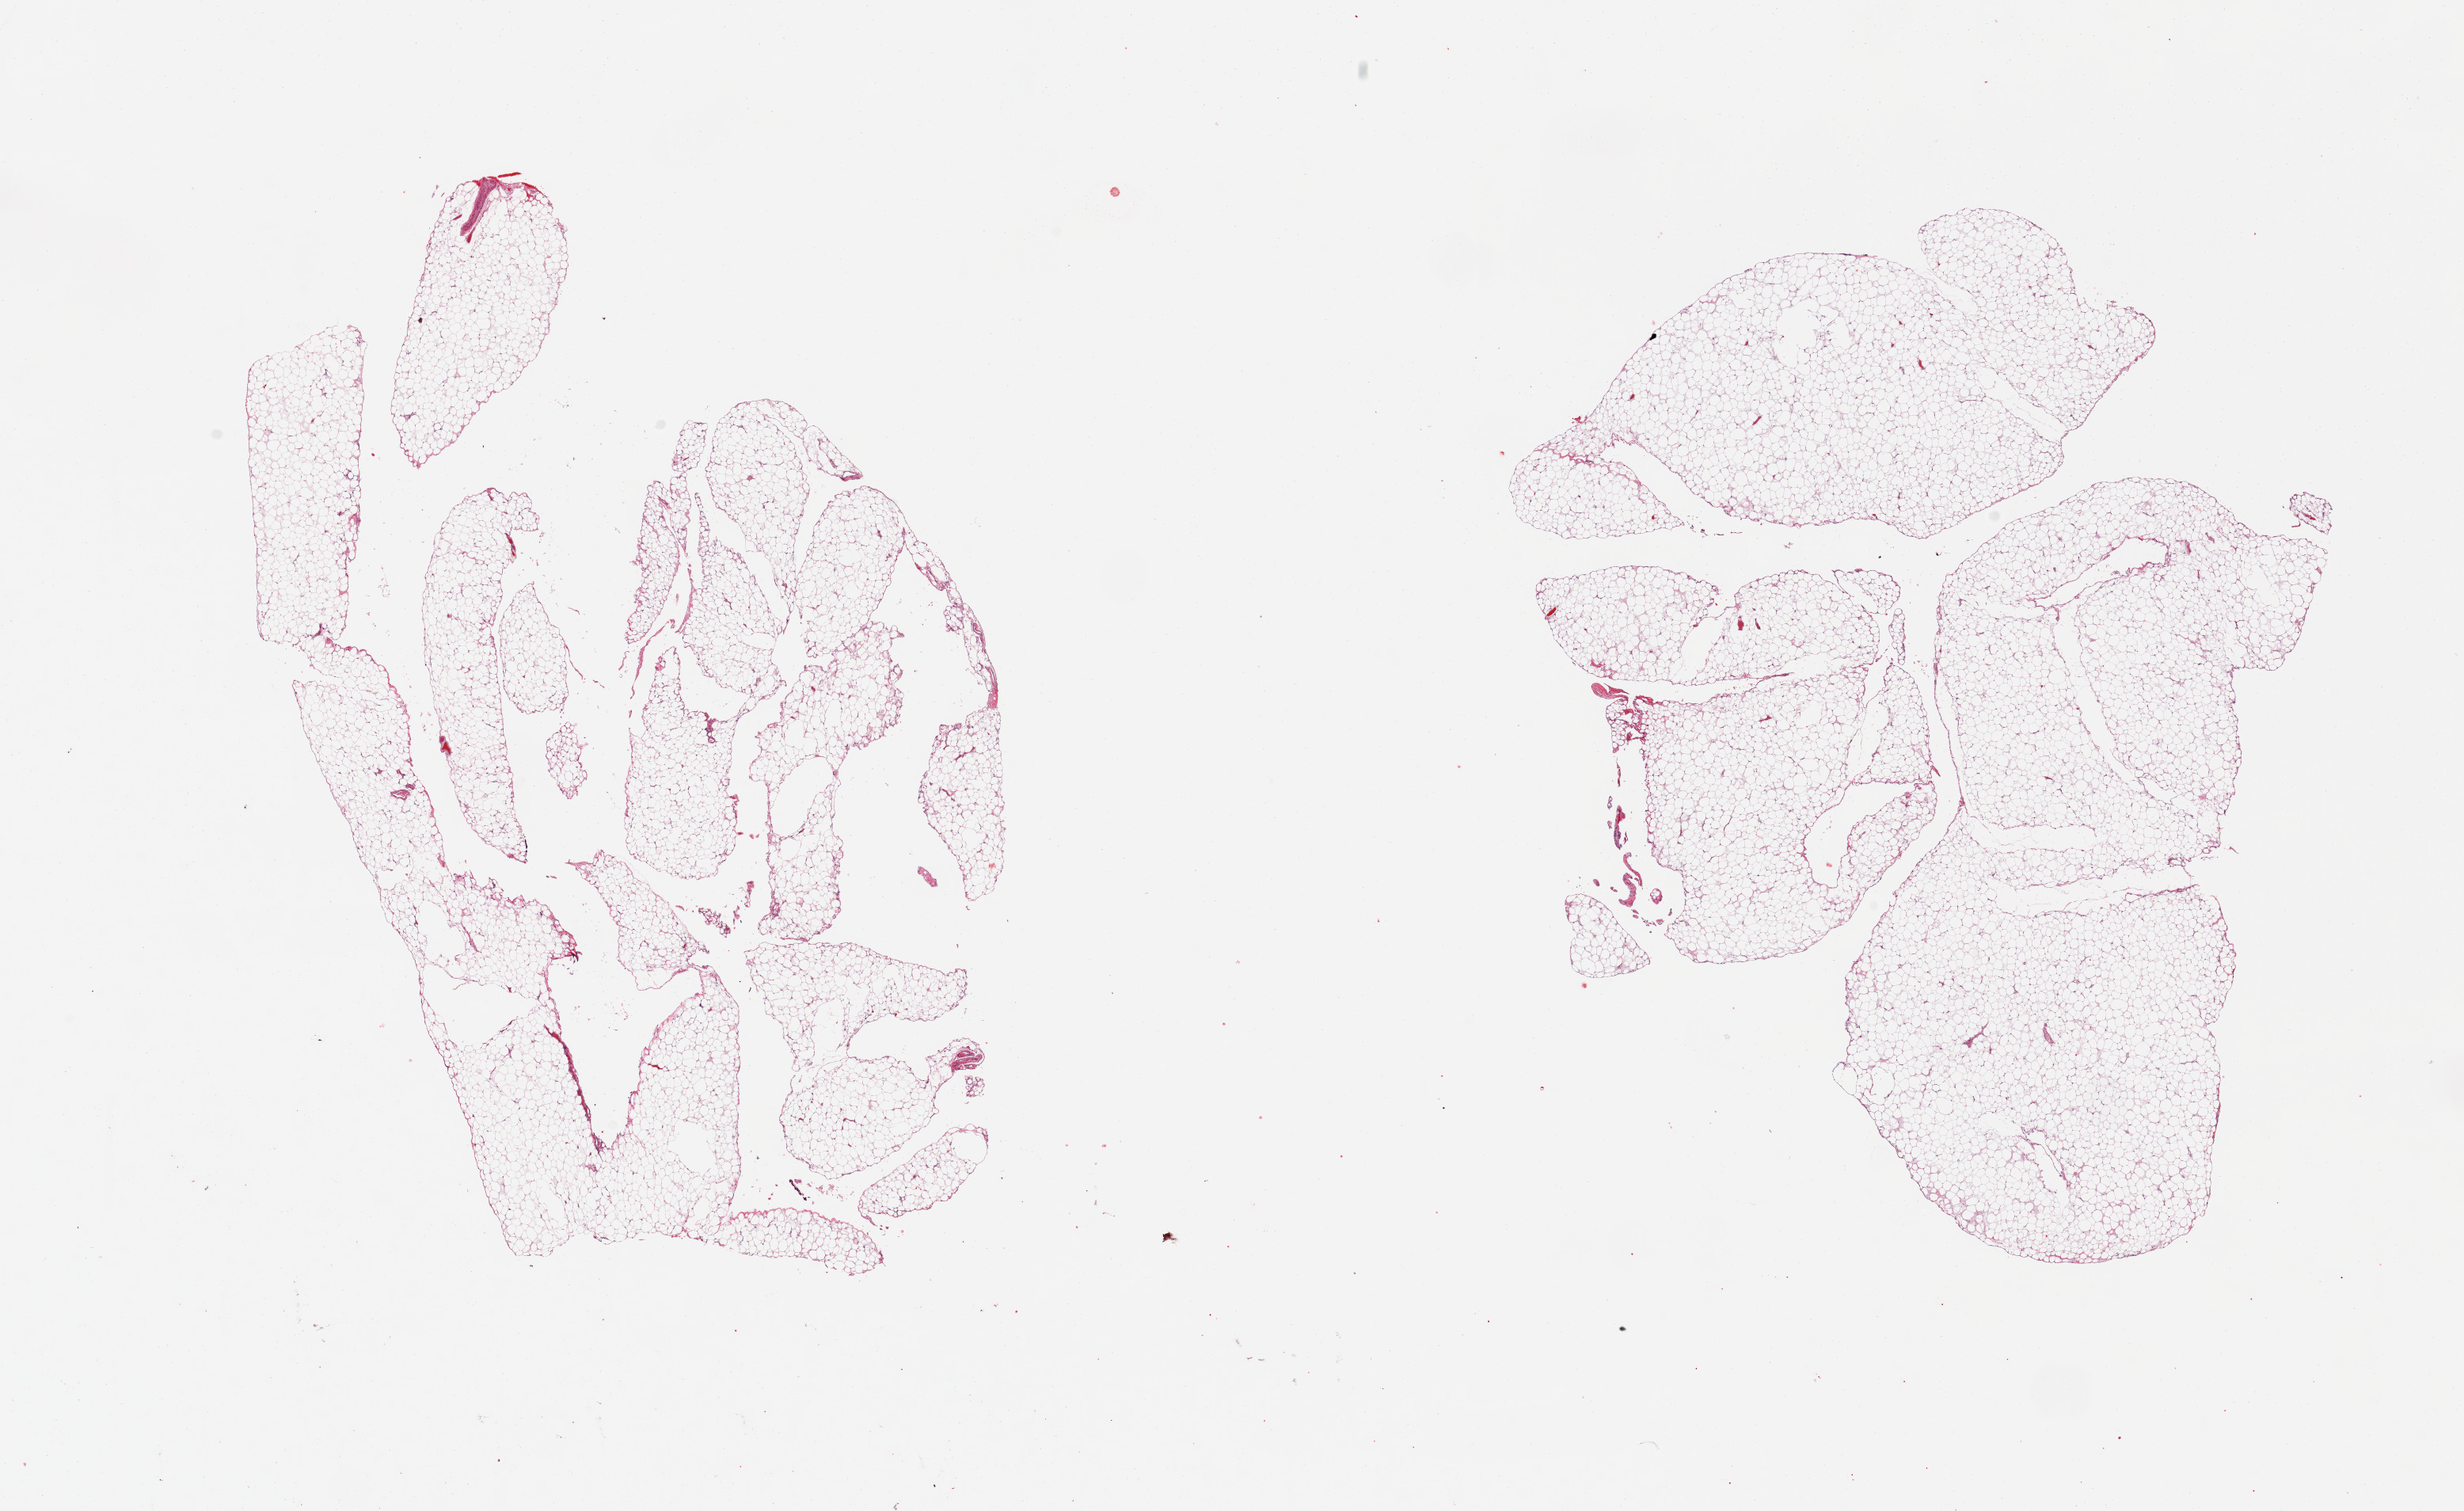
Whole-slide image, hematoxylin and eosin (H&E) stain — shown as a low-resolution overview of the whole scanned area (about 24.6 x 15.1 mm); PAXgene-fixed paraffin-embedded (PFPE) section; sampled site (target tissue): omentum; donor tissue sample.
- review note (as recorded): 2 pieces; minimal stromal content